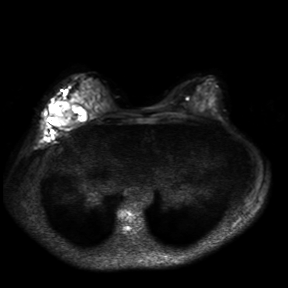
Breast MRI, one axial slice. Slice 17 of 30 in the series (ordered by position). Diffusion-weighted series; image 2 of 4 stored at this slice position (different b-values; order by instance number). 3 T. 4 mm slice thickness. 288 × 288 image matrix, field of view 360 × 360 mm. Female patient.
Structures marked on this image (expert manual segmentation):
- tumour on diffusion-weighted imaging: bounding box (x1, y1, x2, y2) in pixels: (50, 102, 70, 125)